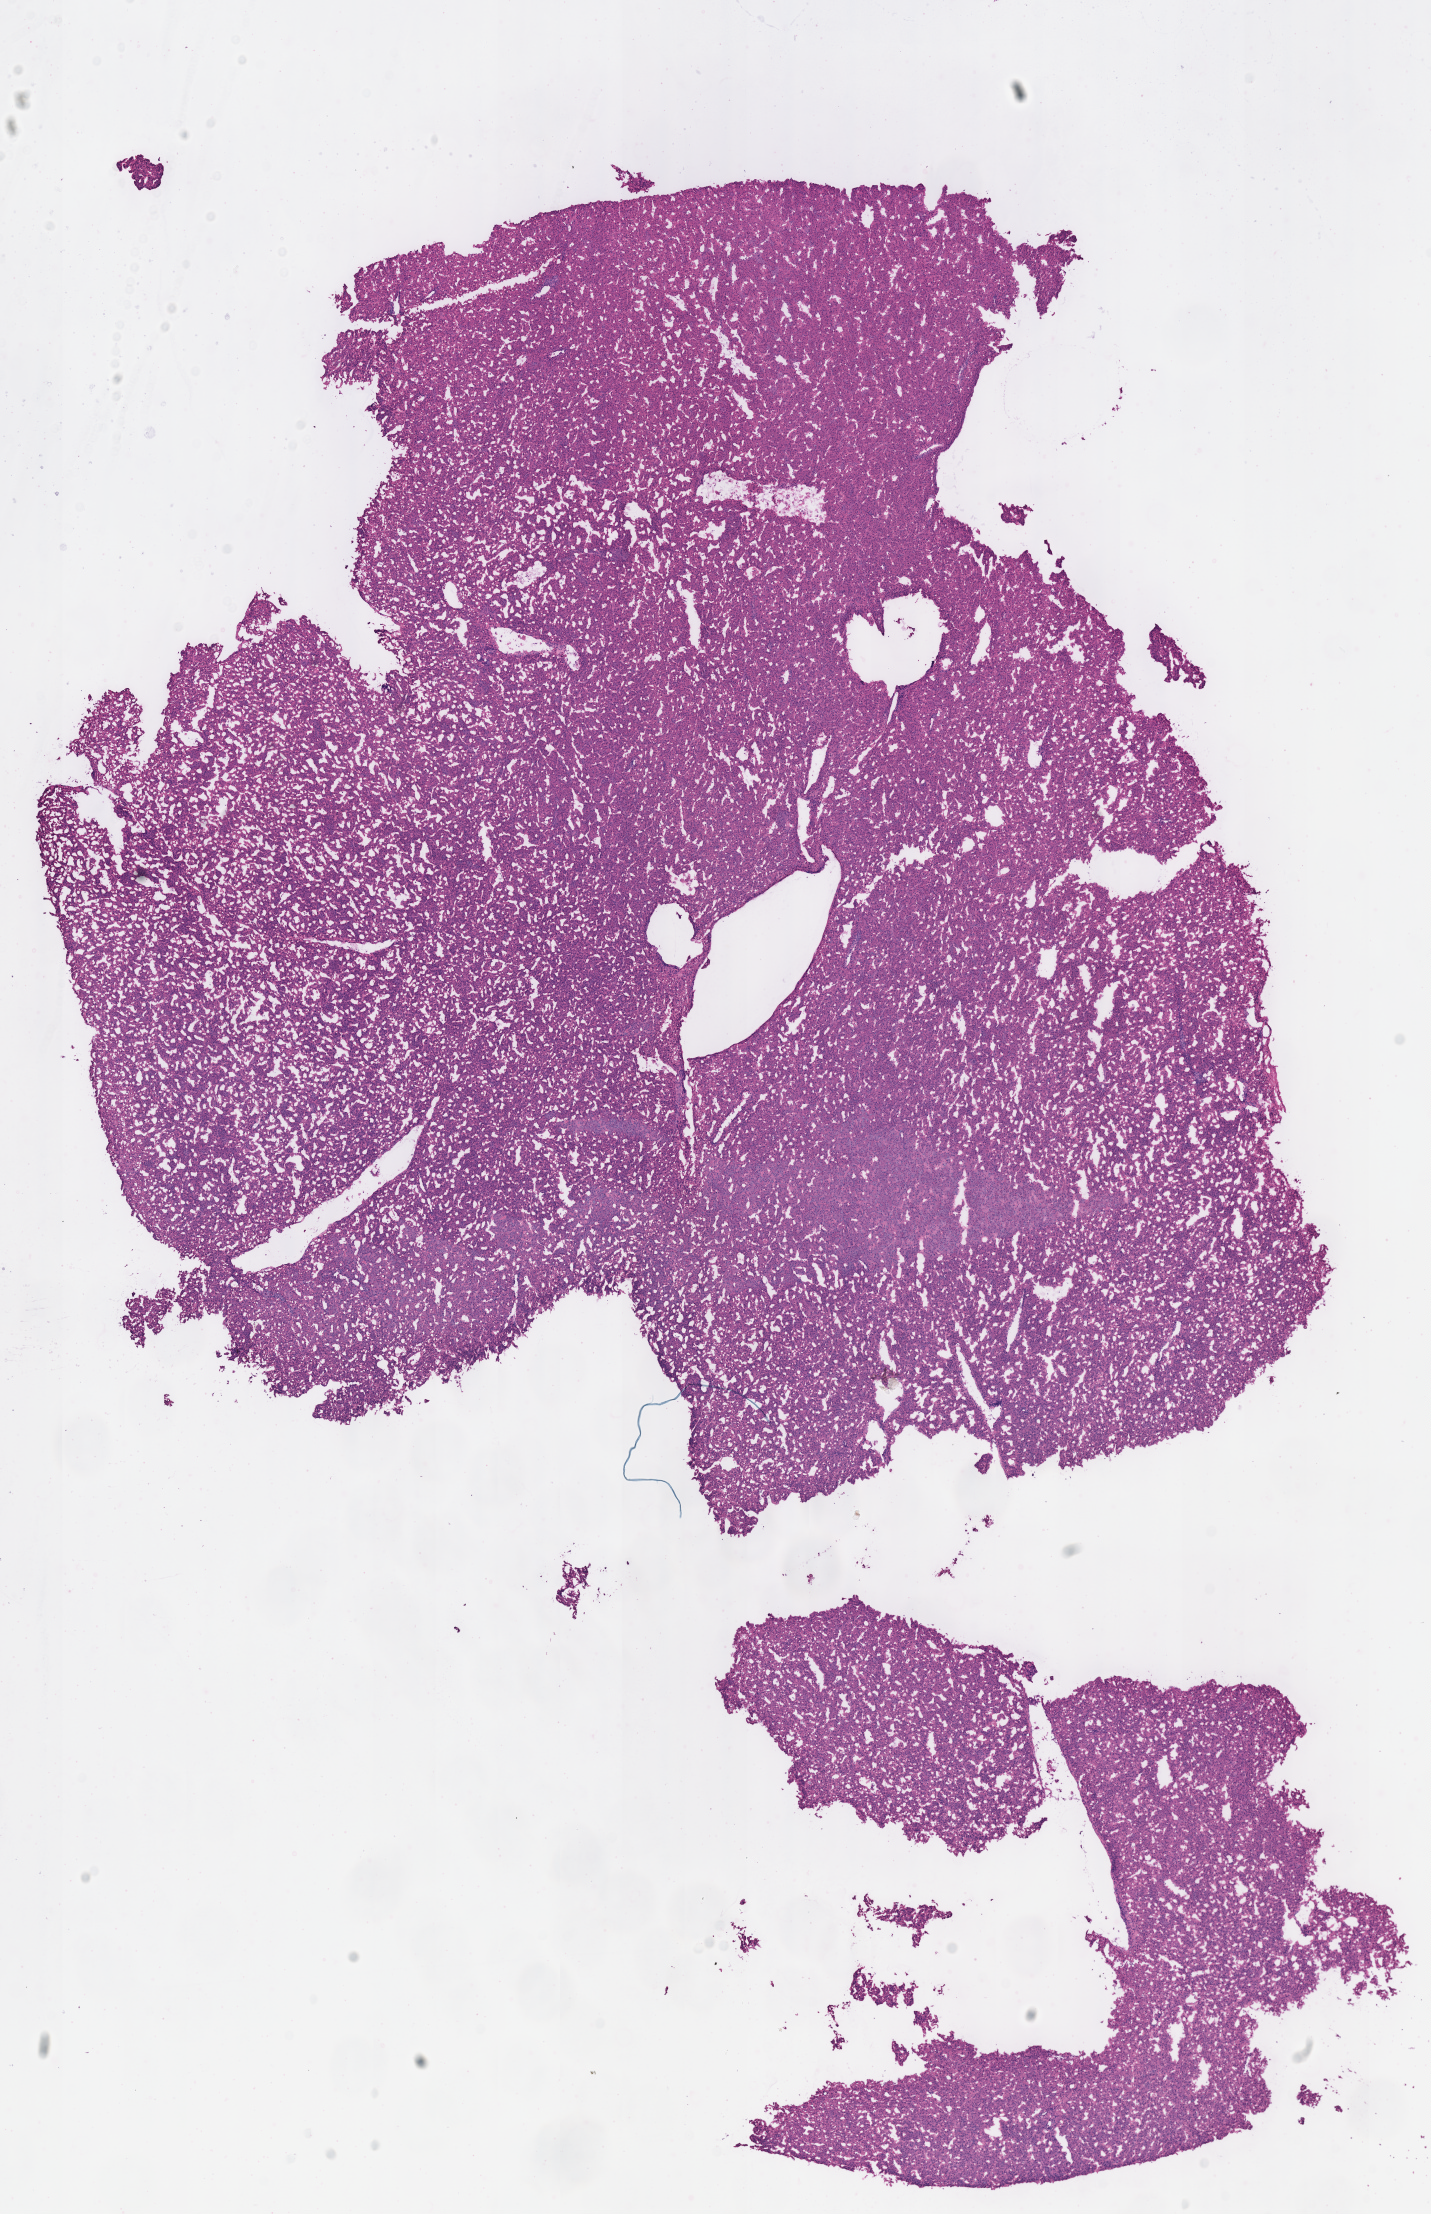
H&E whole-slide image — whole scanned area (about 11.3 x 17.4 mm) shown as a low-resolution overview. Frozen section from the top of the tissue portion. Kidney, primary tumour sample. Male, age 30 years at initial diagnosis. Slide review estimates, as recorded: tumour cells 90%, tumour nuclei 85%, normal cells 0%, stromal cells 10%, necrosis 0%.
- histologic diagnosis: Renal cell carcinoma, chromophobe type
- laterality: left
- AJCC pathologic stage: I (7th edition)